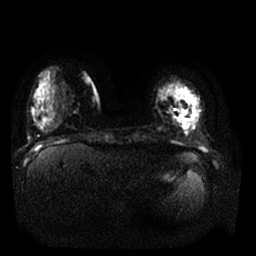
Breast MRI, one axial slice; position 3 of 25 along the scan axis; diffusion-weighted series; image 2 of 4 stored at this slice position (different b-values; order by instance number); 1.5 T; 4 mm slice thickness; 256 × 256 image matrix. Female patient.
Structures marked on this image (outlined manually by an expert reader):
- tumour on diffusion-weighted imaging: box from (x=184, y=122) to (x=187, y=126) px